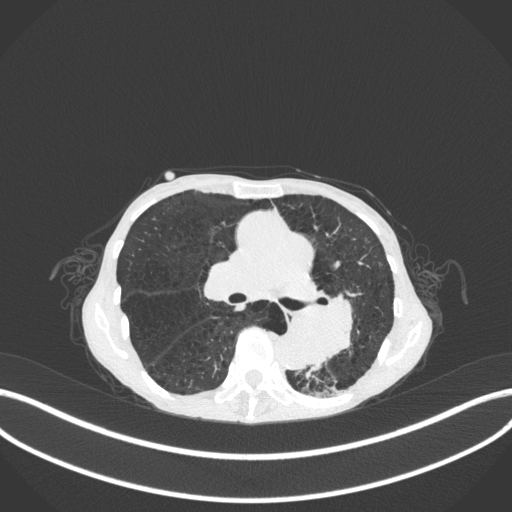
Chest CT, one axial slice. Position 160 of 347 along the scan axis. Reconstruction kernel B31f. 120 kVp. Lung window (W 1500 / L -600 HU). 1 mm slice thickness. 512 × 512 image matrix, field of view 400 × 400 mm. Patient: female, 70 years. Case-level facts recorded for this patient, not image findings: clinical TNM (as recorded): T3 N0 M0.
Annotated regions visible in this slice (rectangle marked by the reading radiologist):
- lung tumour (recorded histology: small cell carcinoma): bounding box [x1, y1, x2, y2] px = [288, 286, 377, 372]